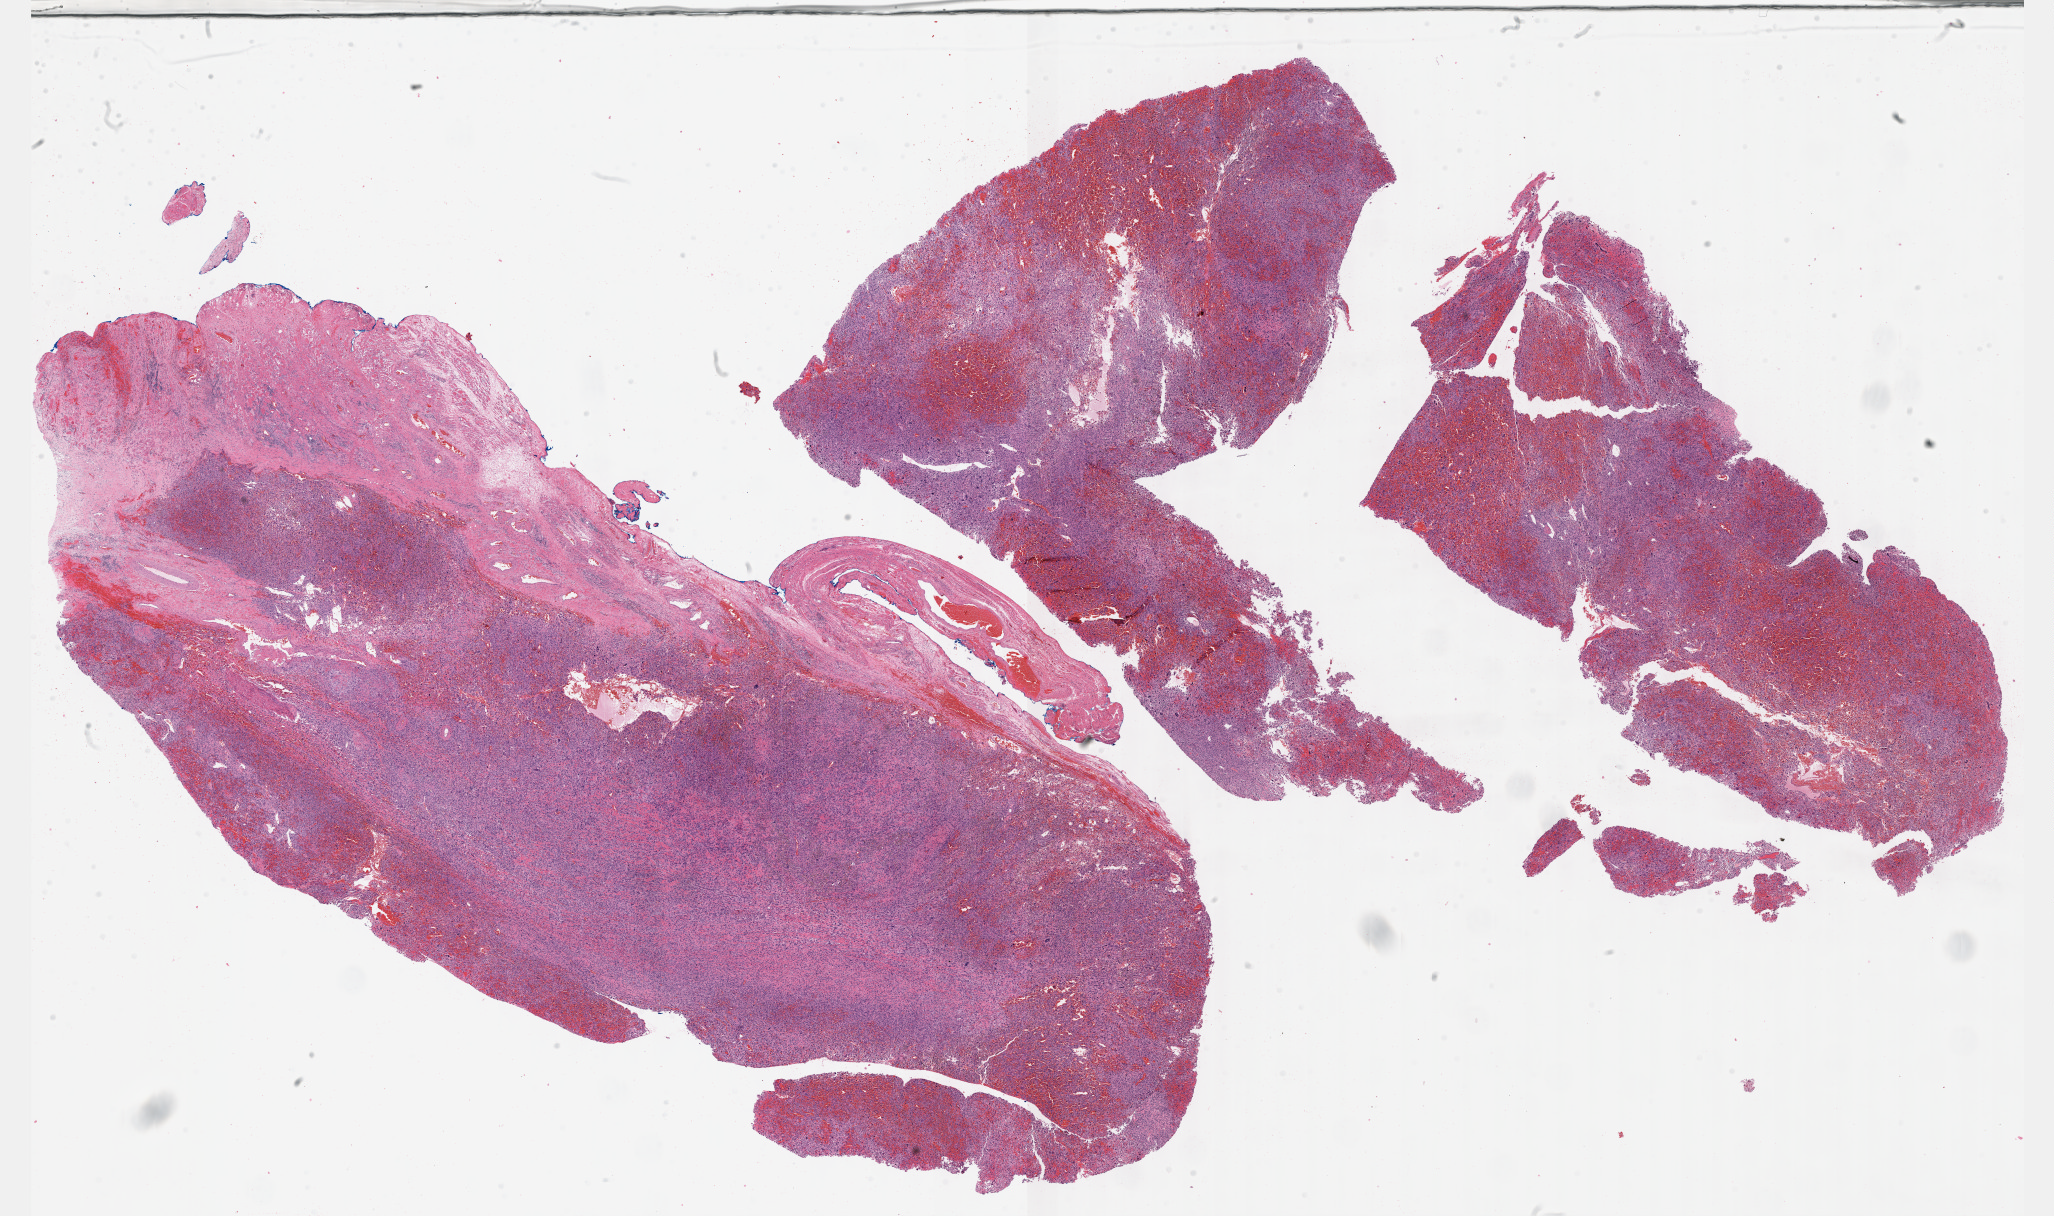
Hematoxylin and eosin (H&E) stained whole-slide image, whole scanned area (about 33.2 x 19.7 mm, slide scanned at 40x) shown as a low-resolution overview; formalin-fixed paraffin-embedded (FFPE) diagnostic section; primary tumour sample from the connective, subcutaneous and other soft tissues. Male patient; age at initial diagnosis 56 years.
Pathologic diagnosis: Undifferentiated sarcoma.